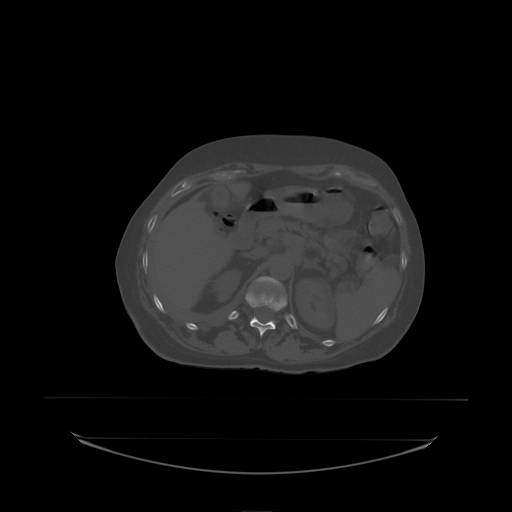
CT including the spine, one axial slice; slice 92 of 242 in the series (ordered by position); bone window (W 1800 / L 400 HU); 2.5 mm slice thickness; 512 × 512 image matrix, field of view 500 × 500 mm. Female patient, age 53 years. From the clinical record (not read from this slice): primary cancer: lung; vertebrae with lytic lesions (as recorded): T7, L1.
Outlined on this slice (semi-automatic segmentation, software-assisted and operator-edited):
- L1 vertebra: box from (x=257, y=277) to (x=284, y=289) px
- T12 vertebra: (x=246, y=292)–(x=287, y=337)